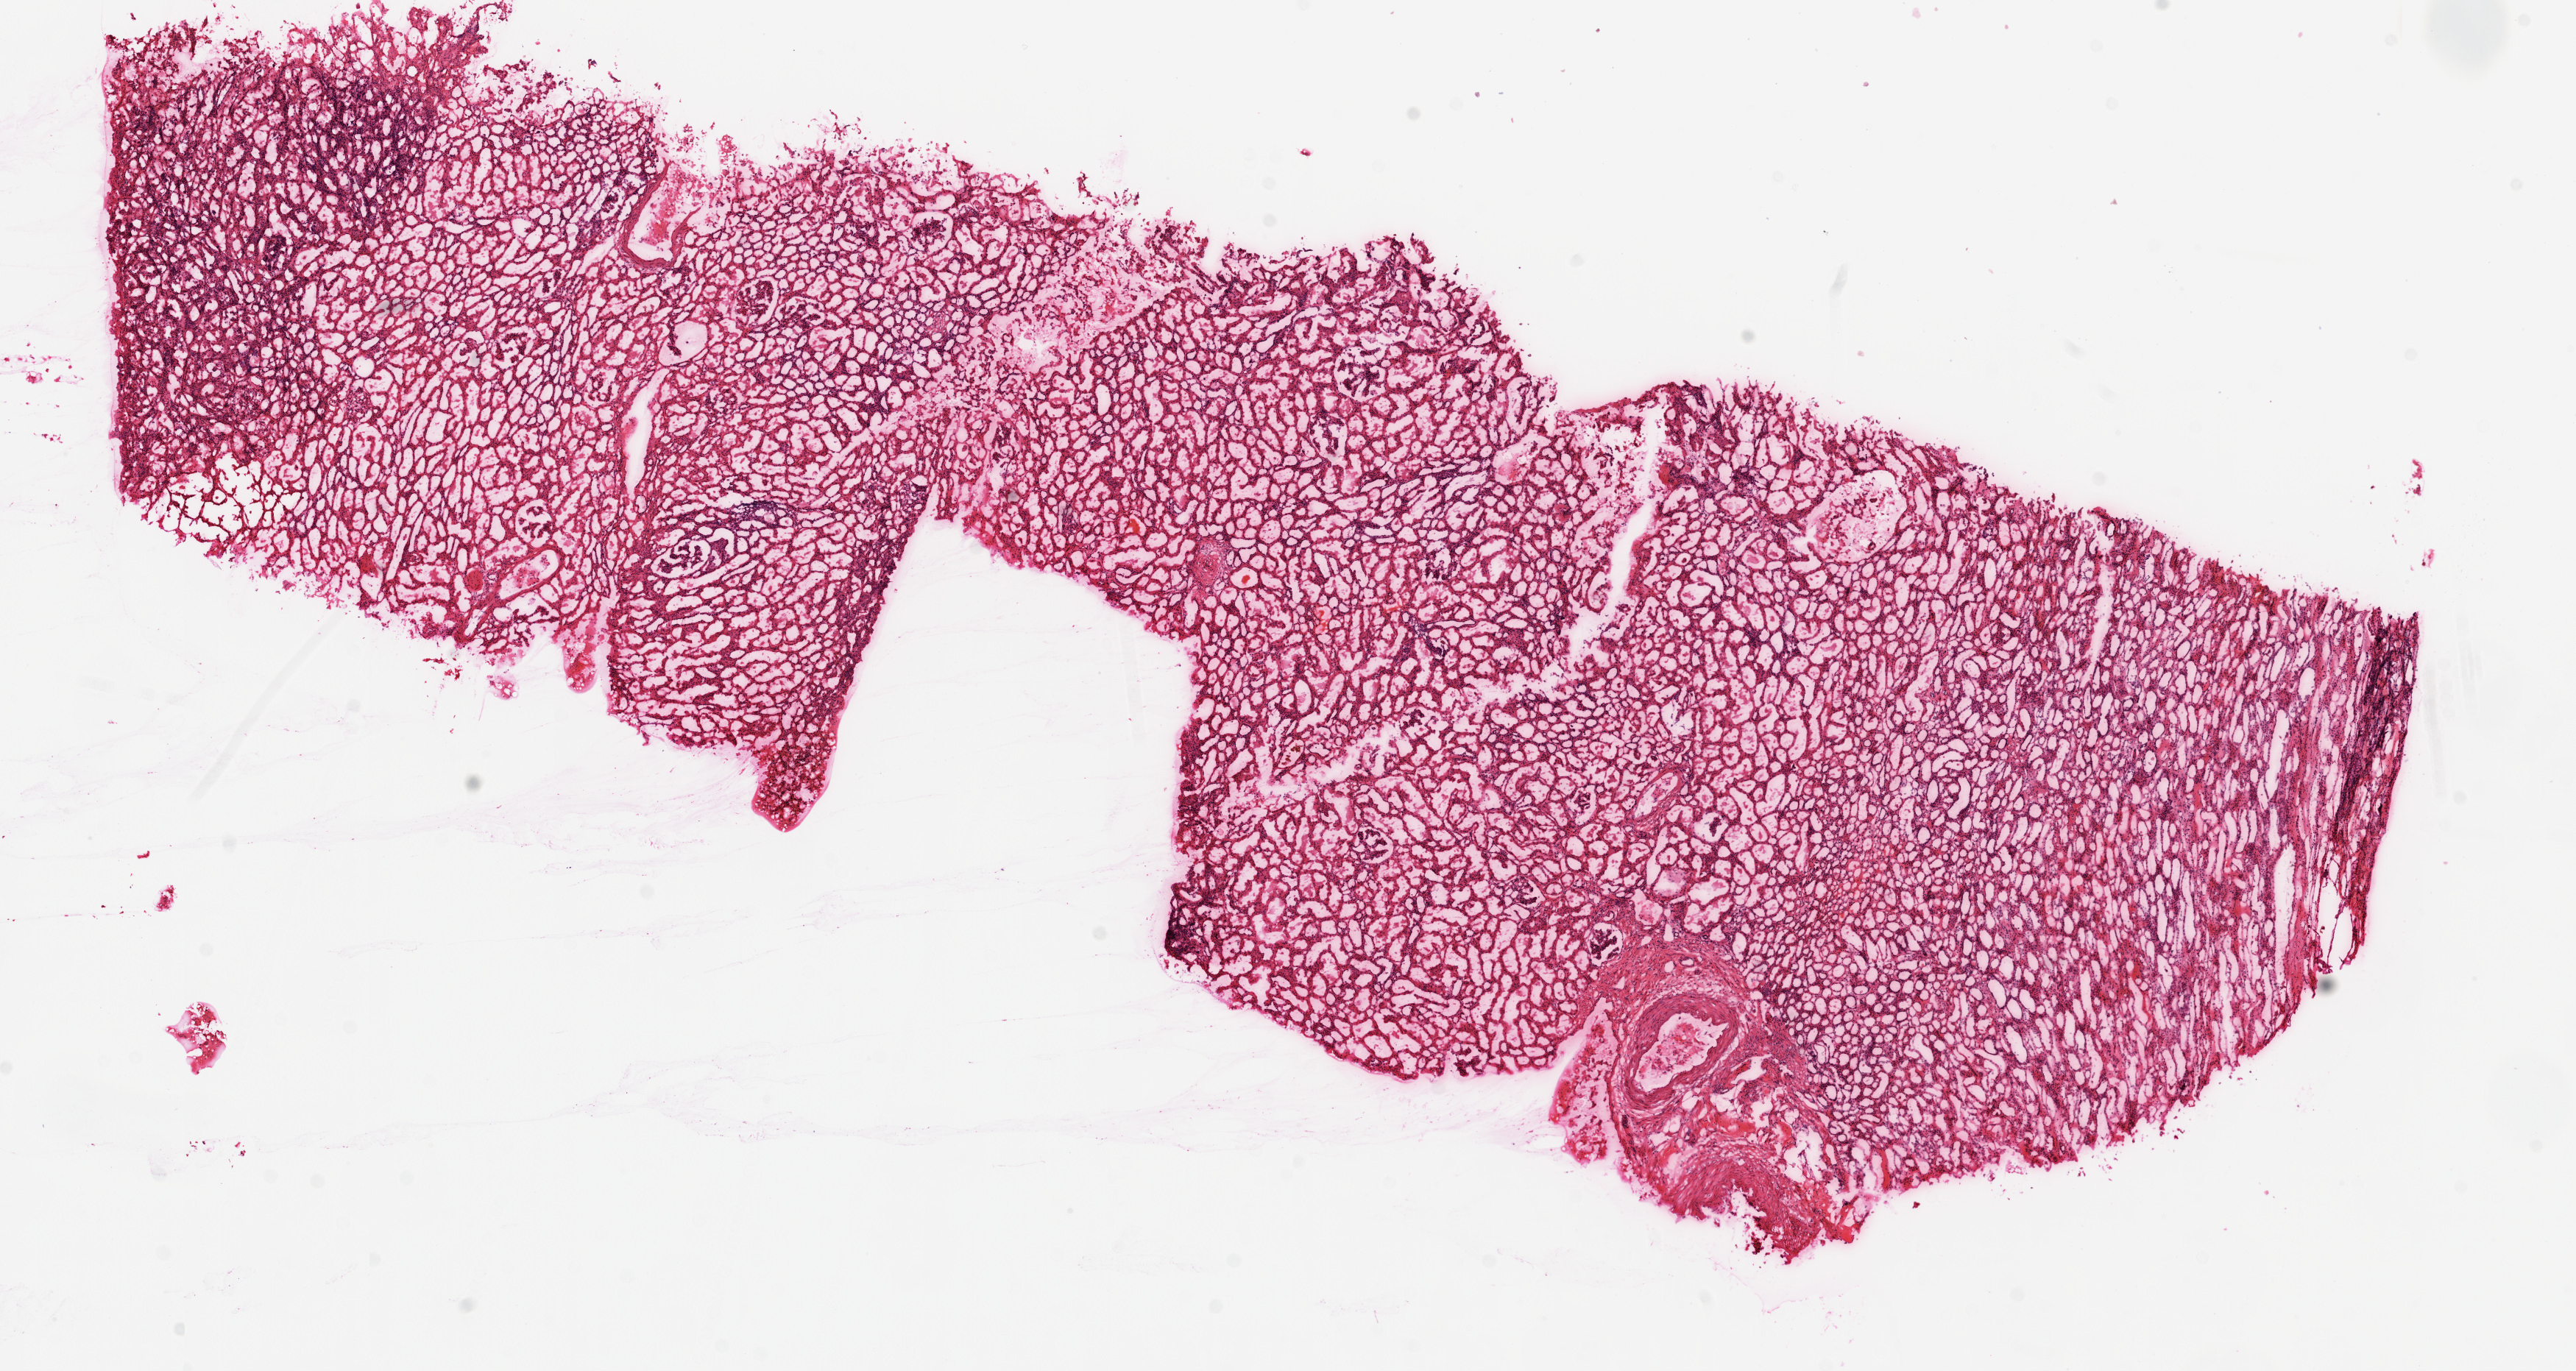
Hematoxylin and eosin (H&E) stained whole-slide image, whole scanned area (about 14.0 x 7.5 mm, acquisition: 20x scan) shown as a low-resolution overview. Frozen section from the top of the tissue portion. Sample: solid tissue normal (non-tumour tissue), kidney. Female patient; age at initial diagnosis 65 years.
This section: solid tissue normal (non-tumour) sample from the same patient. Patient diagnosis: Clear cell adenocarcinoma, NOS.